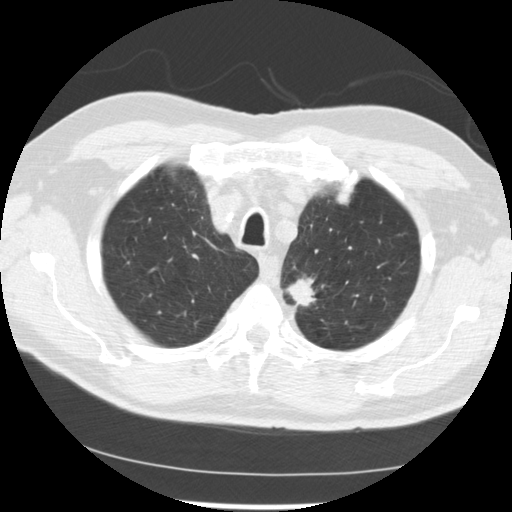
Low-dose screening chest CT, one axial slice. Reconstruction kernel STANDARD. 120 kVp. Lung window (W 1500 / L -600 HU). 2.5 mm slice thickness. 512 × 512 image matrix, field of view 341 × 341 mm.
Structures marked on this image (expert manual segmentation):
- lesion 2 (tumor, upper lobe of left lung): bounding box <287,278,316,307> (left, top, right, bottom; pixels)